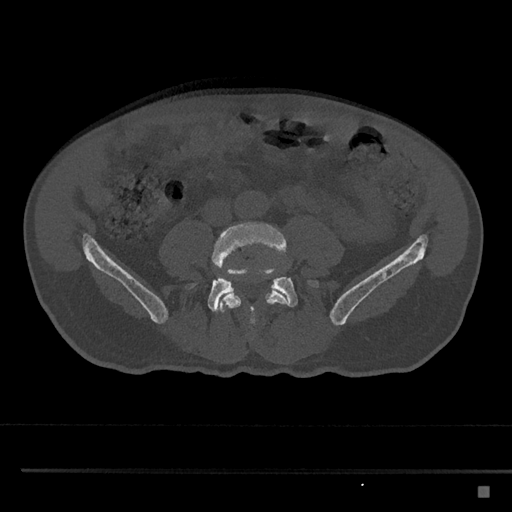
CT including the spine, one axial slice; slice 607 of 797 in the series (ordered by position); 120 kVp; bone window (W 1800 / L 400 HU); 0.5 mm slice thickness; 512 × 512 image matrix. Male patient, age 59 years. From the clinical record (not read from this slice): primary cancer: prostate.
Structures marked on this image (semi-automatically segmented with operator editing):
- L4 vertebra: box from (x=212, y=222) to (x=289, y=332) px
- L5 vertebra: (x=185, y=261)–(x=320, y=313)